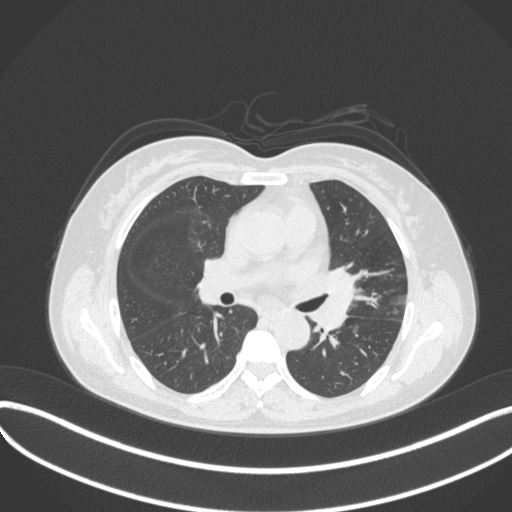
Chest CT, one axial slice; position 195 of 373 along the scan axis; lung window (W 1500 / L -600 HU); 1 mm slice thickness; 512 × 512 image matrix, field of view 400 × 400 mm. Female patient, age 54 years. Case-level facts recorded for this patient, not image findings: clinical TNM (as recorded): T2a N1 M0; histopathological grade: G3.
Structures marked on this image (bounding box drawn by a radiologist):
- lung tumour (recorded histology: small cell carcinoma): bounding box <308,265,359,342> (left, top, right, bottom; pixels)